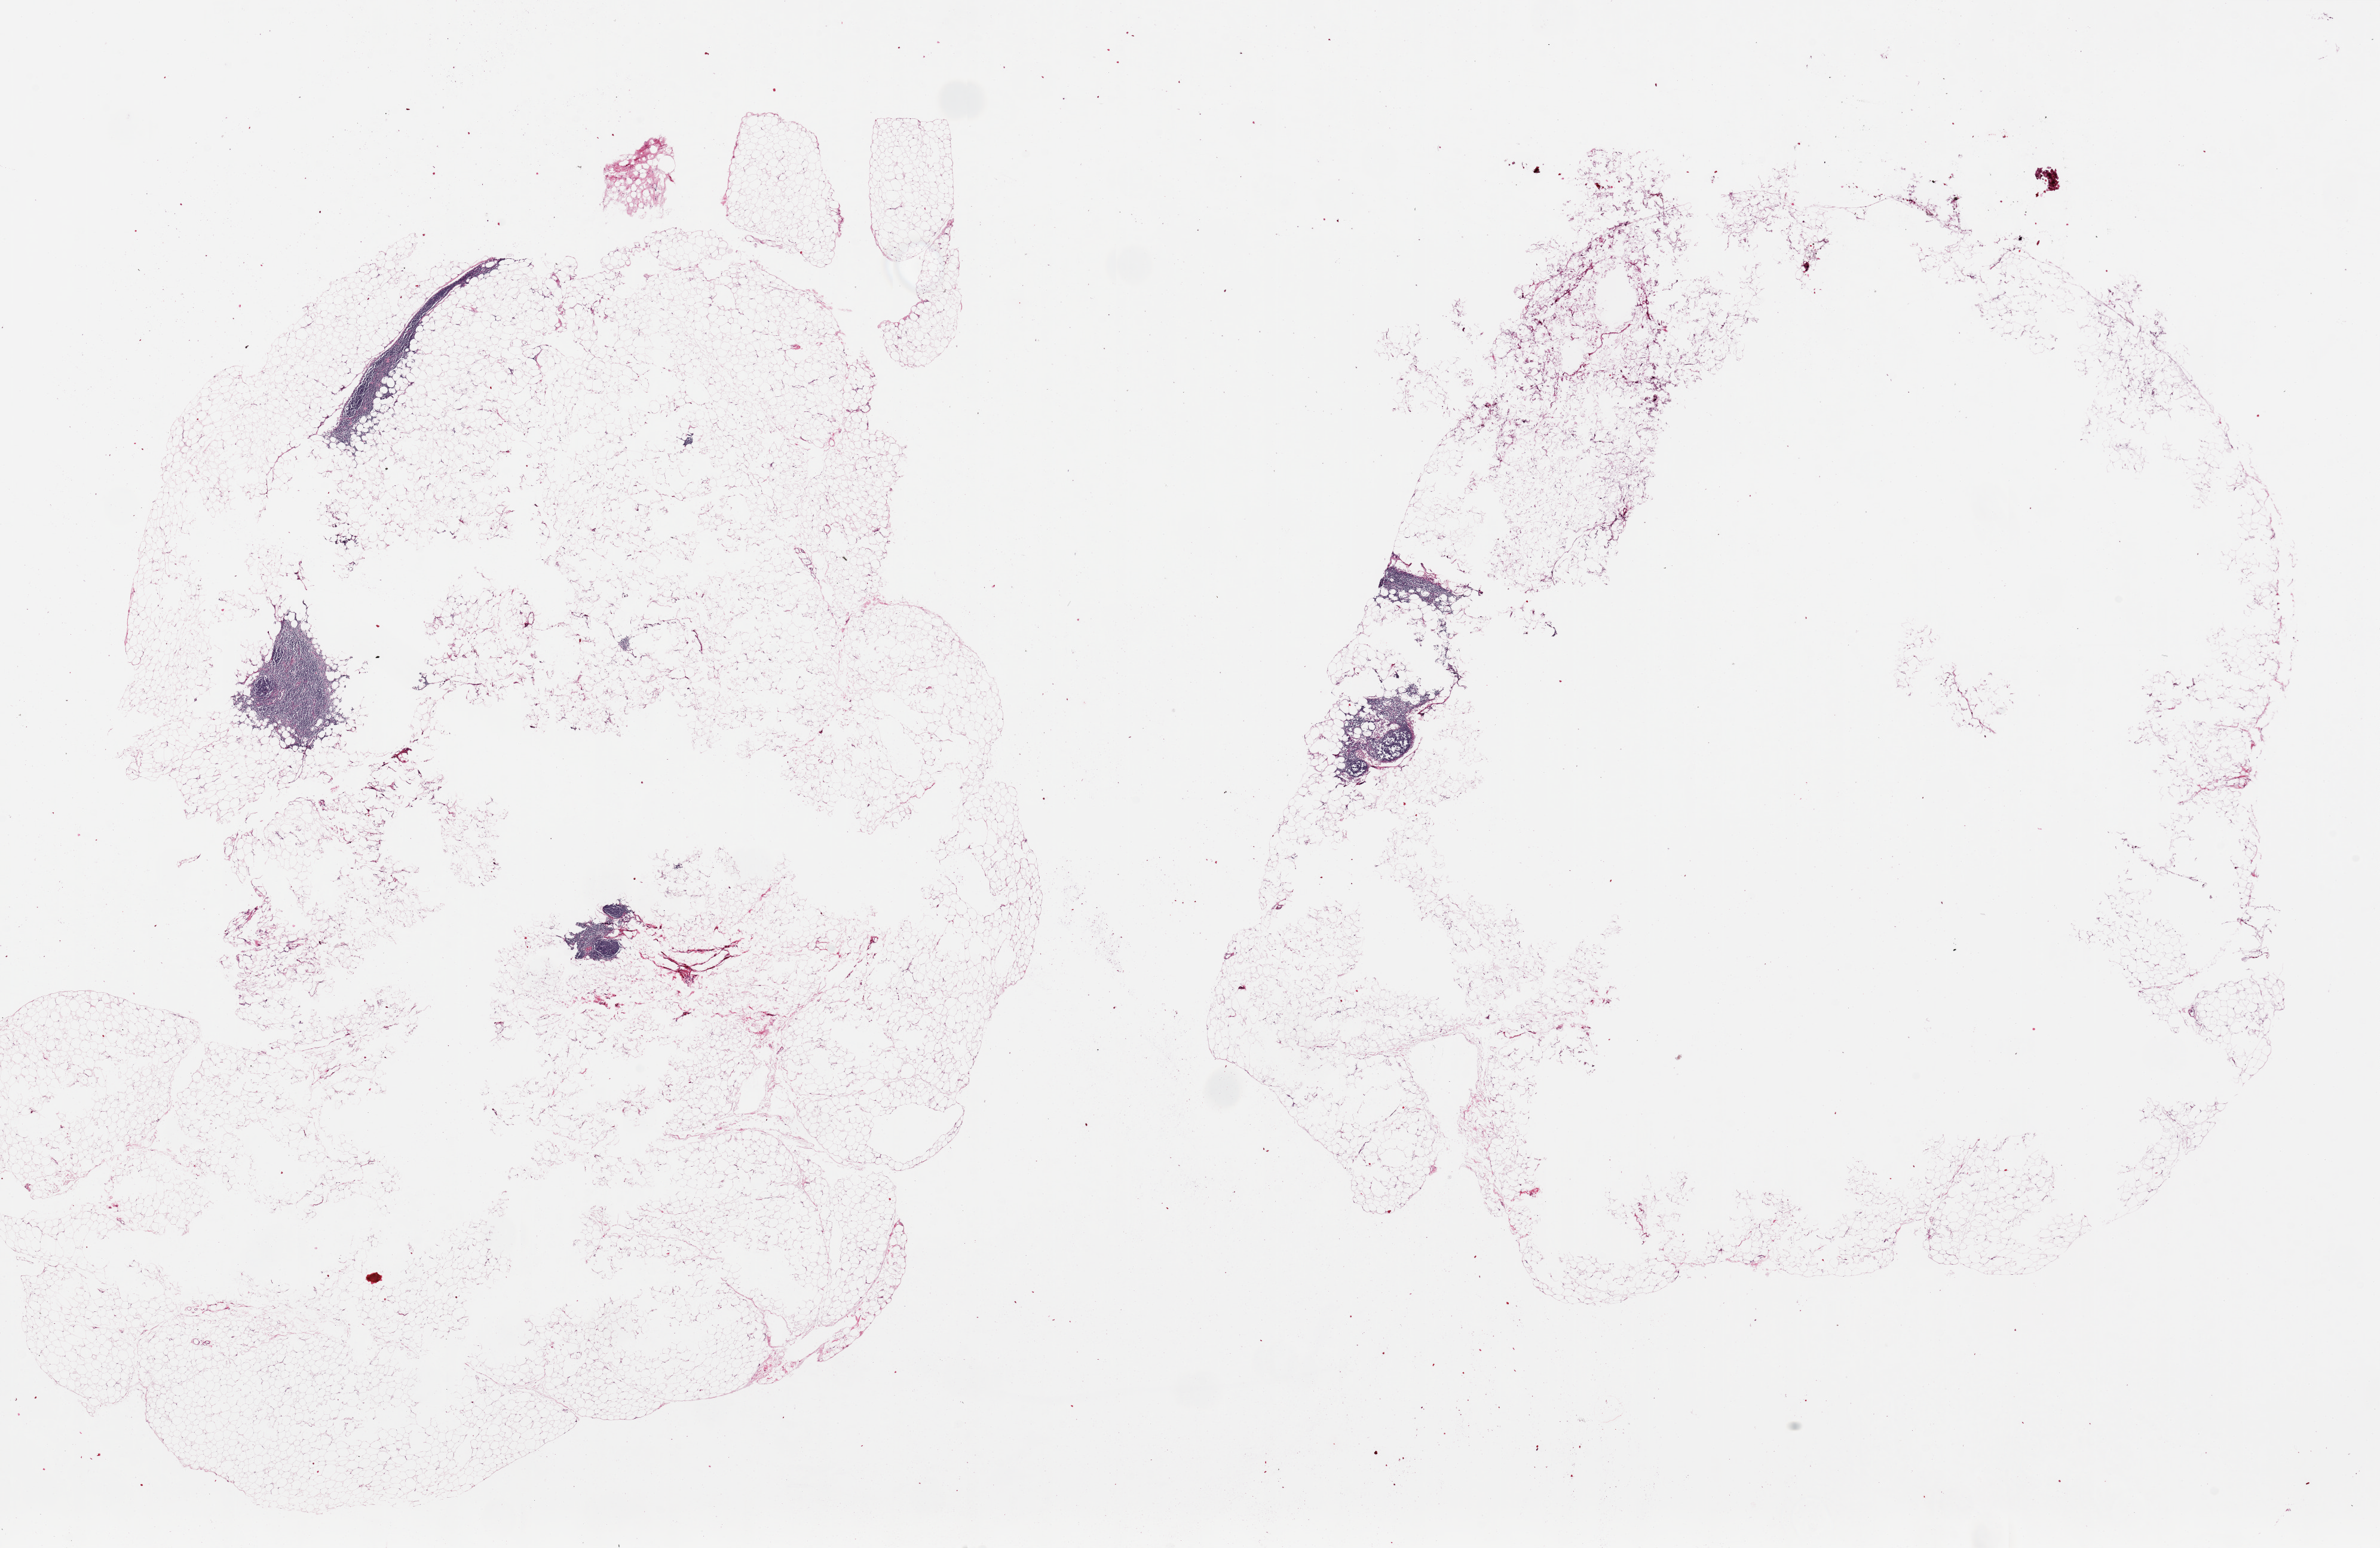
Digitized H&E-stained section, brightfield — whole scanned area (about 31.5 x 20.5 mm) shown as a low-resolution overview. PAXgene-fixed paraffin-embedded (PFPE) section. Target tissue: omentum. Tissue donor sample. Donor: male.
Review note (as recorded): 2 pieces ~15x12mm; Patch lymphoid aggregates; Poorly fixed.